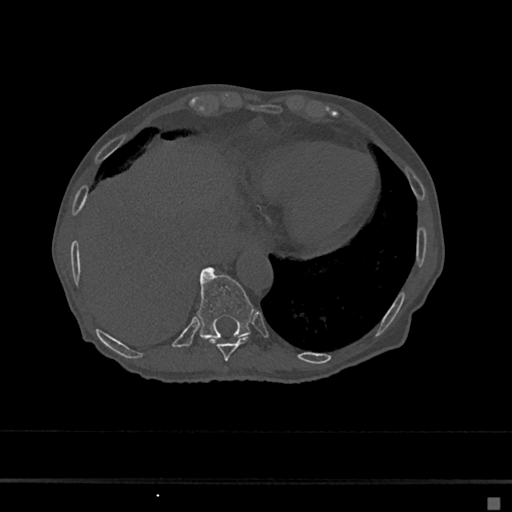
CT including the spine, one axial slice. Position 245 of 797 along the scan axis. Reconstruction kernel Br40s/3. 120 kVp. Bone window (W 1800 / L 400 HU). 512 × 512 image matrix, field of view 360 × 360 mm. Patient: female, 68 years. From the clinical record (not read from this slice): primary cancer: renal.
Outlined on this slice (semi-automatically segmented with operator editing):
- T10 vertebra: bounding box <197,268,253,339> (left, top, right, bottom; pixels)
- T9 vertebra: <209,336,249,361>